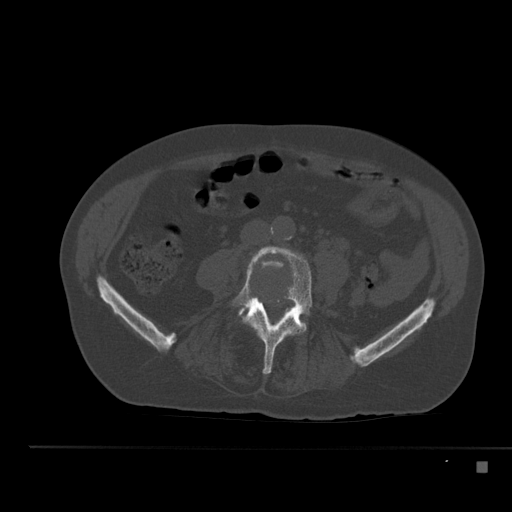
CT including the spine, one axial slice. Slice 141 of 517 in the series (ordered by position). Bone window (W 1800 / L 400 HU). 1.5 mm slice thickness. 512 × 512 image matrix, field of view 408 × 408 mm. Male patient, age 70 years. Case-level facts recorded for this patient, not image findings: primary cancer: renal.
Structures marked on this image (semi-automatic segmentation, software-assisted and operator-edited):
- L4 vertebra: bounding box (x1, y1, x2, y2) in pixels: (232, 245, 313, 374)
- L5 vertebra: (239, 306, 247, 316)